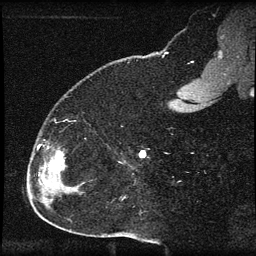
Breast MRI (dynamic contrast-enhanced), one sagittal slice; position 20 of 60 along the scan axis; dynamic contrast-enhanced series, image 2 of 3 at this slice position (ordered by acquisition); 1.5 T; TE 4.2 ms, TR 8.2 ms; 2 mm slice thickness; 256 × 256 image matrix, field of view 180 × 180 mm. Patient: female, 32 years.
Structures marked on this image (semi-automatically segmented with operator editing):
- analysis volume of interest (the breast-tissue region the enhancement analysis was run in; not a lesion): bounding box <31,139,67,184> (left, top, right, bottom; pixels)
- tumour enhancement mask (voxels above the 70 % enhancement threshold inside the analysis volume of interest): <38,145,64,184>